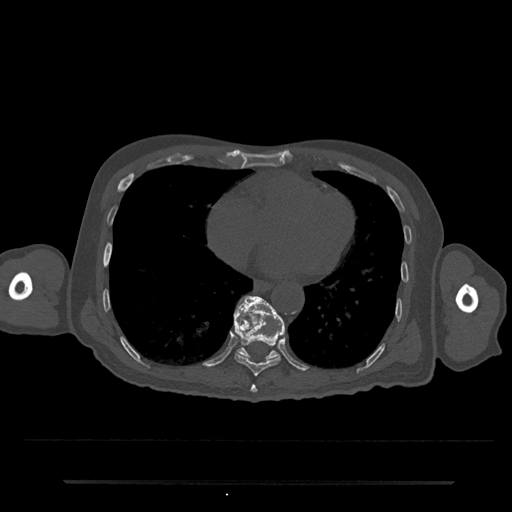
CT including the spine, one axial slice; position 350 of 797 along the scan axis; reconstruction kernel Br40s/3; 120 kVp; bone window (W 1800 / L 400 HU); 0.5 mm slice thickness; 512 × 512 image matrix, field of view 427 × 427 mm. Male patient, age 74 years. Case-level facts recorded for this patient, not image findings: primary cancer: prostate.
Structures marked on this image (semi-automatically segmented with operator editing):
- T10 vertebra: bounding box <235,296,285,360> (left, top, right, bottom; pixels)
- T8 vertebra: <250,385,258,393>
- T9 vertebra: <234,296,285,376>